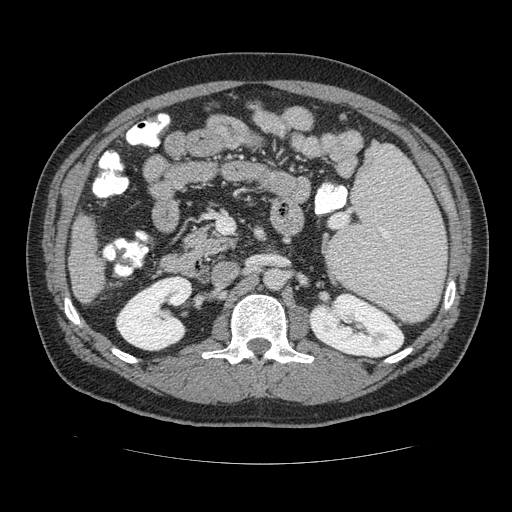
Contrast-enhanced abdominal CT (liver protocol), one axial slice. Slice 53 of 113 in the series (ordered by position). Soft-tissue window (W 400 / L 40 HU). 2.5 mm slice thickness. 512 × 512 image matrix, field of view 400 × 400 mm. Case-level facts recorded for this patient, not image findings: diagnosis: hepatocellular carcinoma (patient treated with transarterial chemoembolisation; whether this scan precedes or follows treatment is not stated here); TNM stage (as recorded): Stage-II; Child-Pugh class: B; tumour differentiation: moderately differentiated.
Annotated regions visible in this slice (semi-automatically segmented with operator editing):
- liver parenchyma outside the tumour (the mass and vessels are separate outlines, so this box may not span the whole liver): bounding box <66,210,106,306> (left, top, right, bottom; pixels)